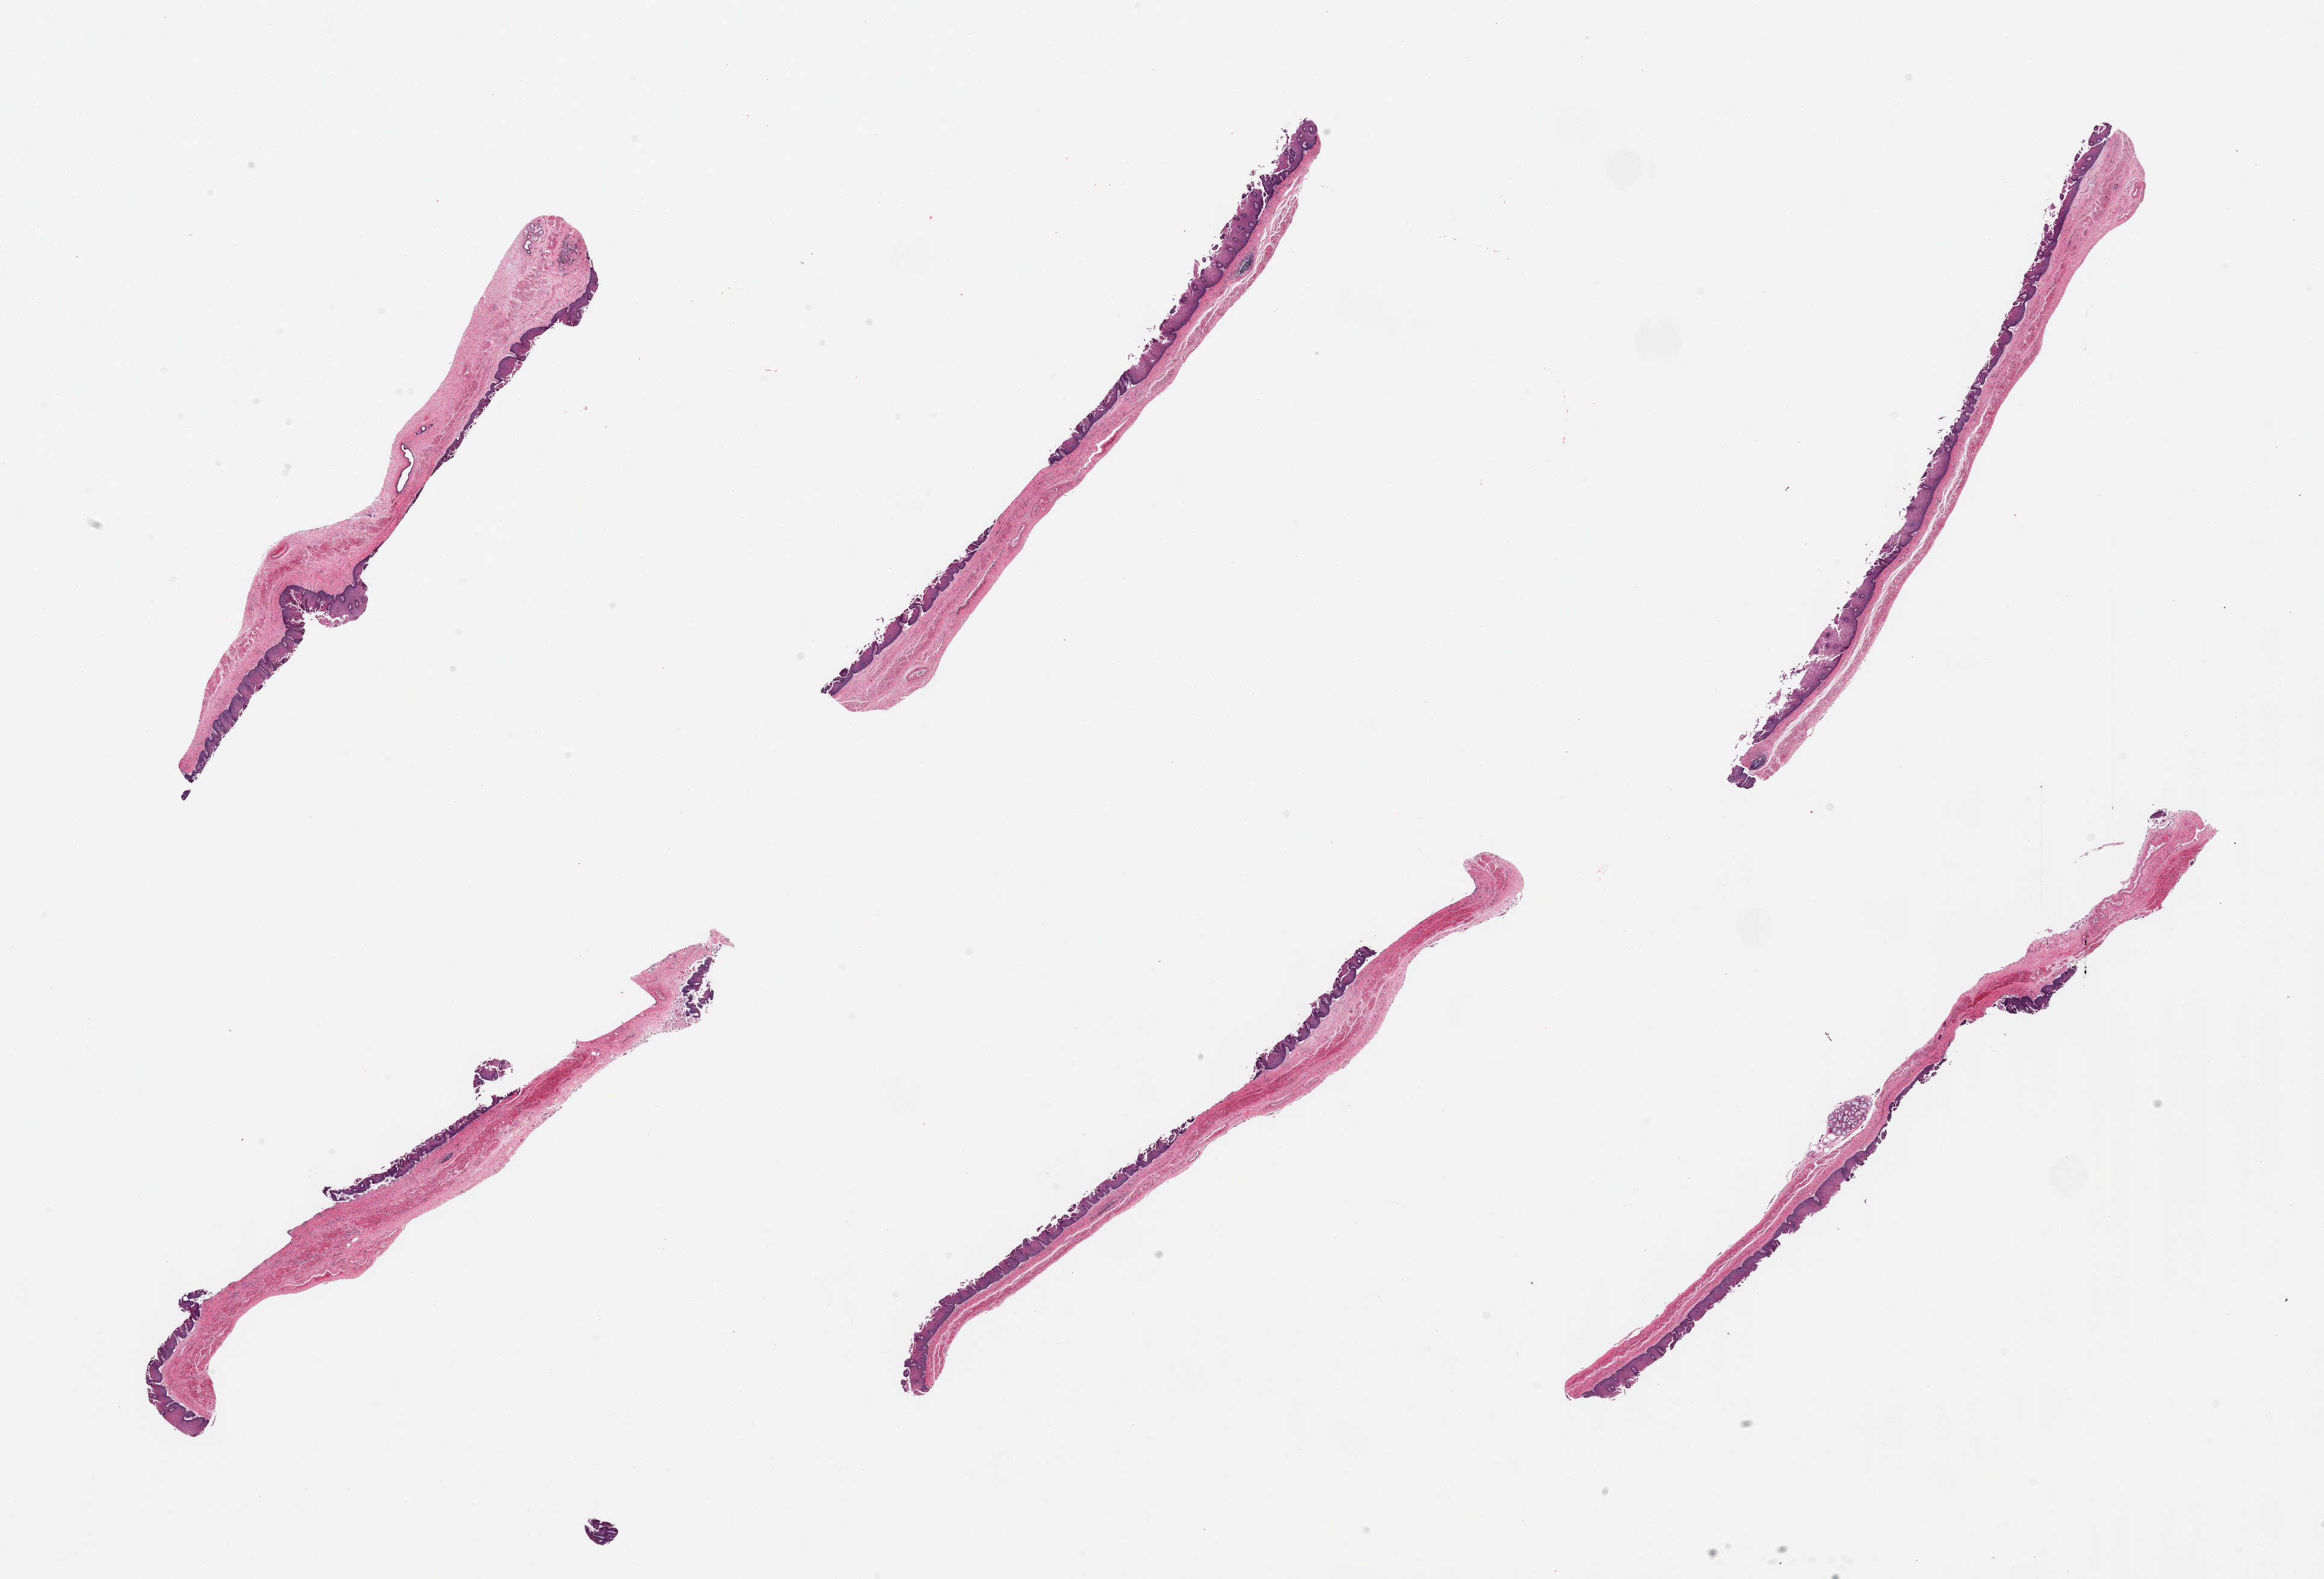
Haematoxylin and eosin whole-slide image, brightfield — a low-resolution overview of the entire scanned area, about 30.5 x 20.7 mm (from a 20x scan). PAXgene-fixed paraffin-embedded (PFPE) section. Section of esophageal mucous membrane (target tissue). Donor tissue sample. Male donor.
Pathologist's review note for this sample: 6 pieces, squamous mucosa up to ~0.2mm, ~30-40% thickness, unusually advance autolysis, partially sloughing.